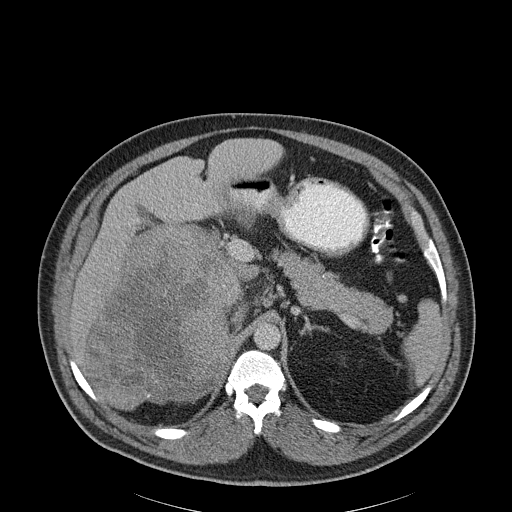
Contrast-enhanced abdominal CT, one axial slice; position 137 of 186 along the scan axis; 120 kVp; soft-tissue window (W 400 / L 40 HU); 3 mm slice thickness; 512 × 512 image matrix, field of view 464 × 464 mm. Patient: male, 56 years. Case-level facts recorded for this patient, not image findings: diagnosis: adrenocortical carcinoma; tumour side: right adrenal; tumour size at pathology: 18 cm; Ki-67 index: 2 %; stage (as recorded): 3.
Annotated regions visible in this slice (semi-automatically segmented with operator editing):
- mass: bounding box [x1, y1, x2, y2] px = [85, 227, 241, 407]